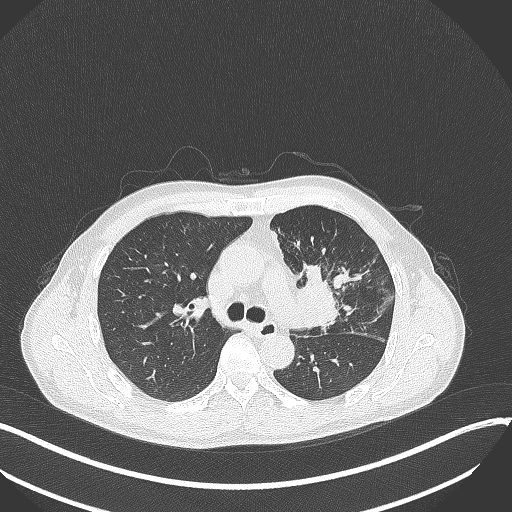
Chest CT, one axial slice; position 220 of 411 along the scan axis; reconstruction kernel B70f; 120 kVp; lung window (W 1500 / L -600 HU); 1 mm slice thickness; 512 × 512 image matrix, field of view 400 × 400 mm. Male patient, age 56 years. Case-level facts recorded for this patient, not image findings: clinical TNM (as recorded): T2a N0 M0.
Outlined on this slice (rectangle marked by the reading radiologist):
- lung tumour (recorded histology: squamous cell carcinoma): bounding box (x1, y1, x2, y2) in pixels: (294, 261, 342, 333)